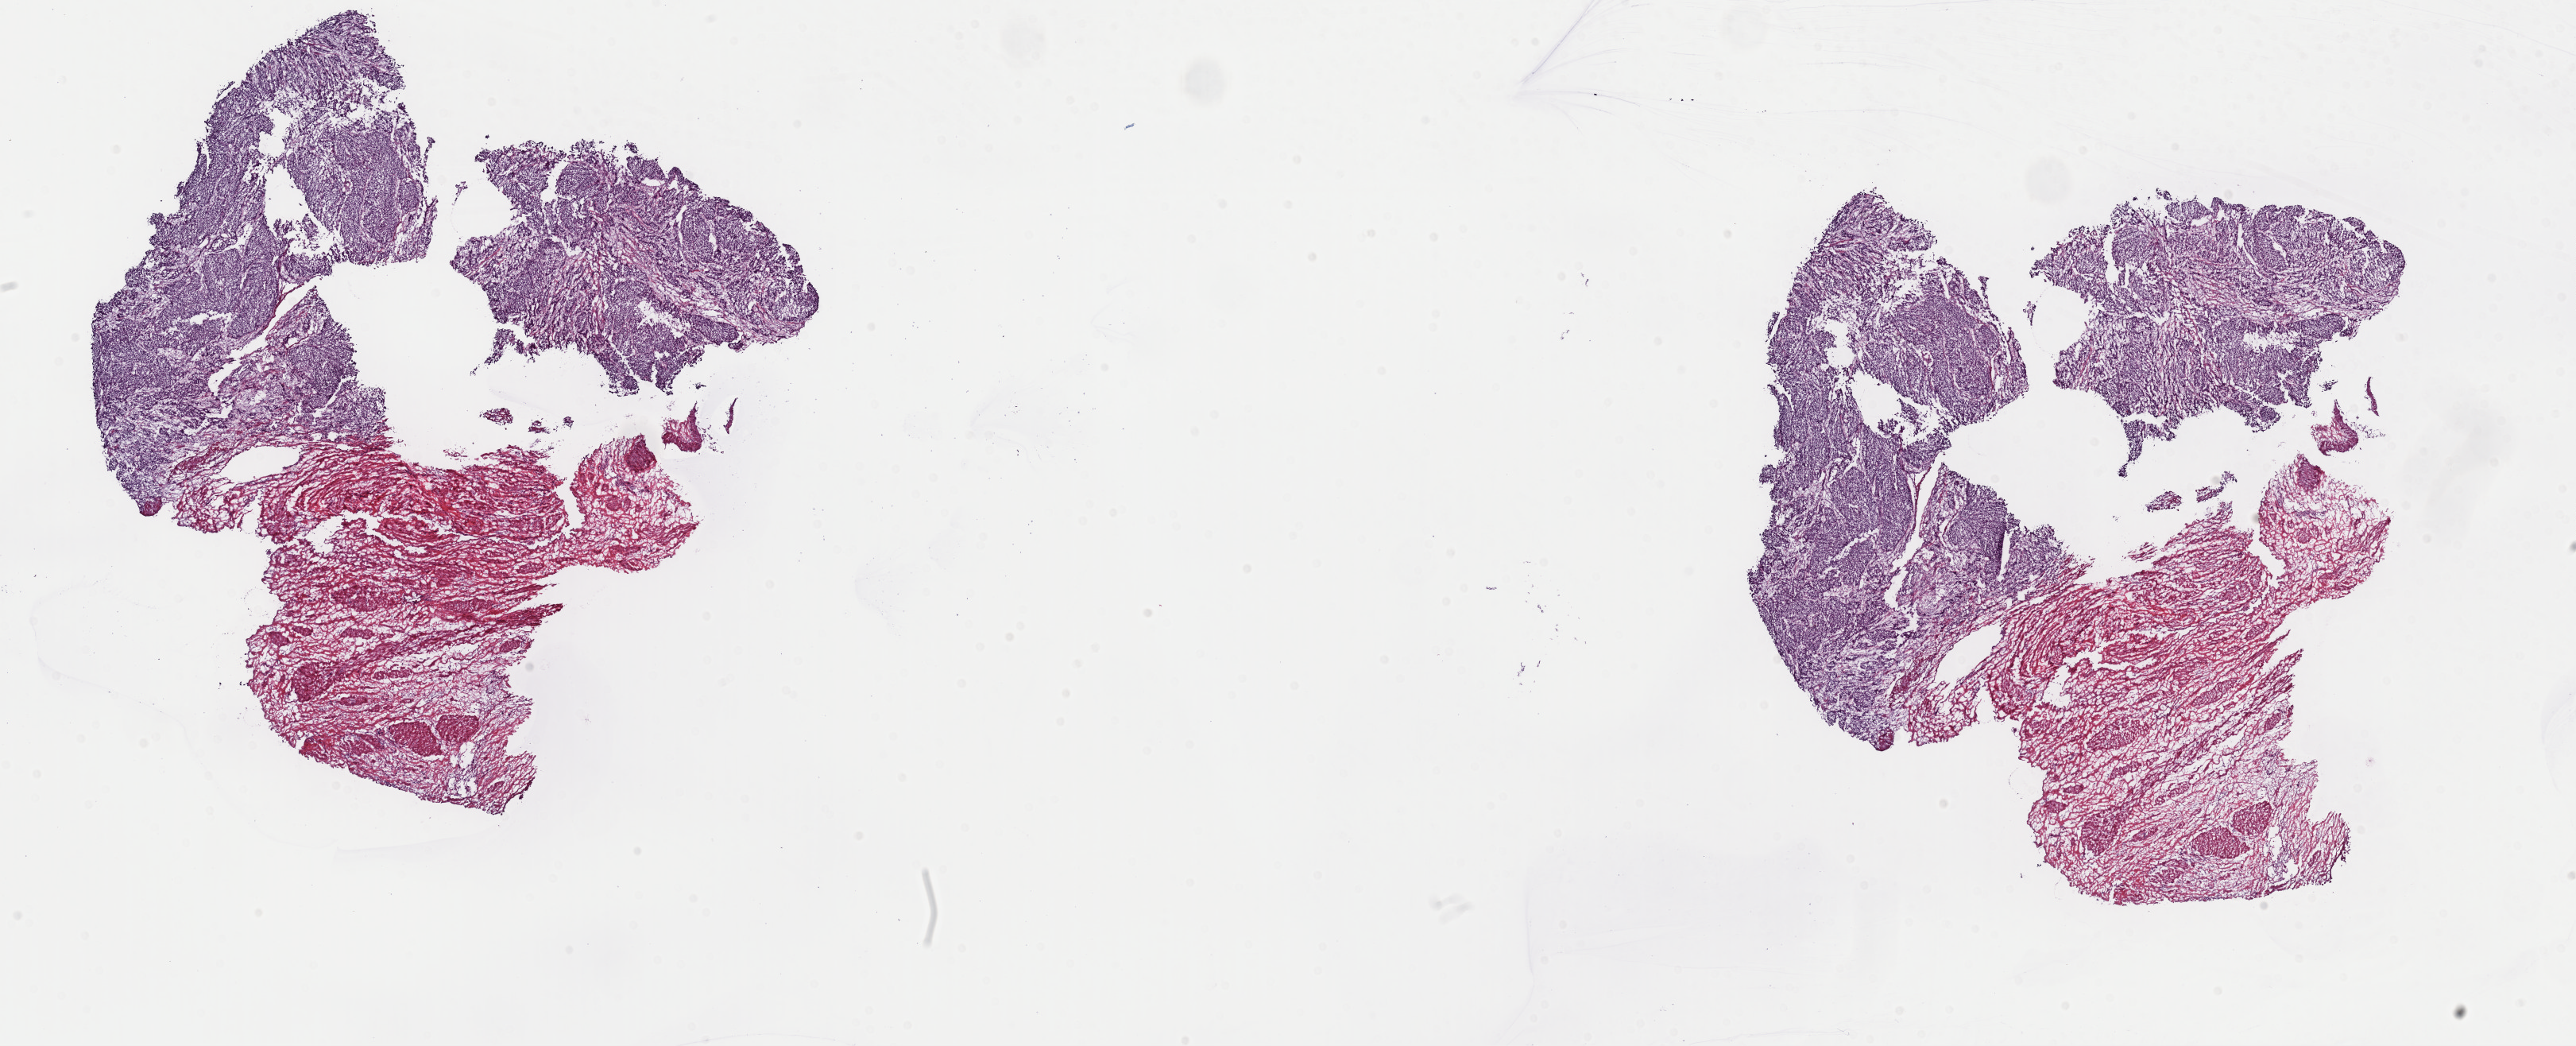
Whole-slide histology image, Hematoxylin and eosin (H&E) stained, shown as a low-resolution overview of the whole scanned area (about 25.6 x 10.4 mm, from a 40x scan), frozen section from the top of the tissue portion, bladder, primary tumour sample. Male, age 78 years at initial diagnosis.
Histologic diagnosis: Transitional cell carcinoma.